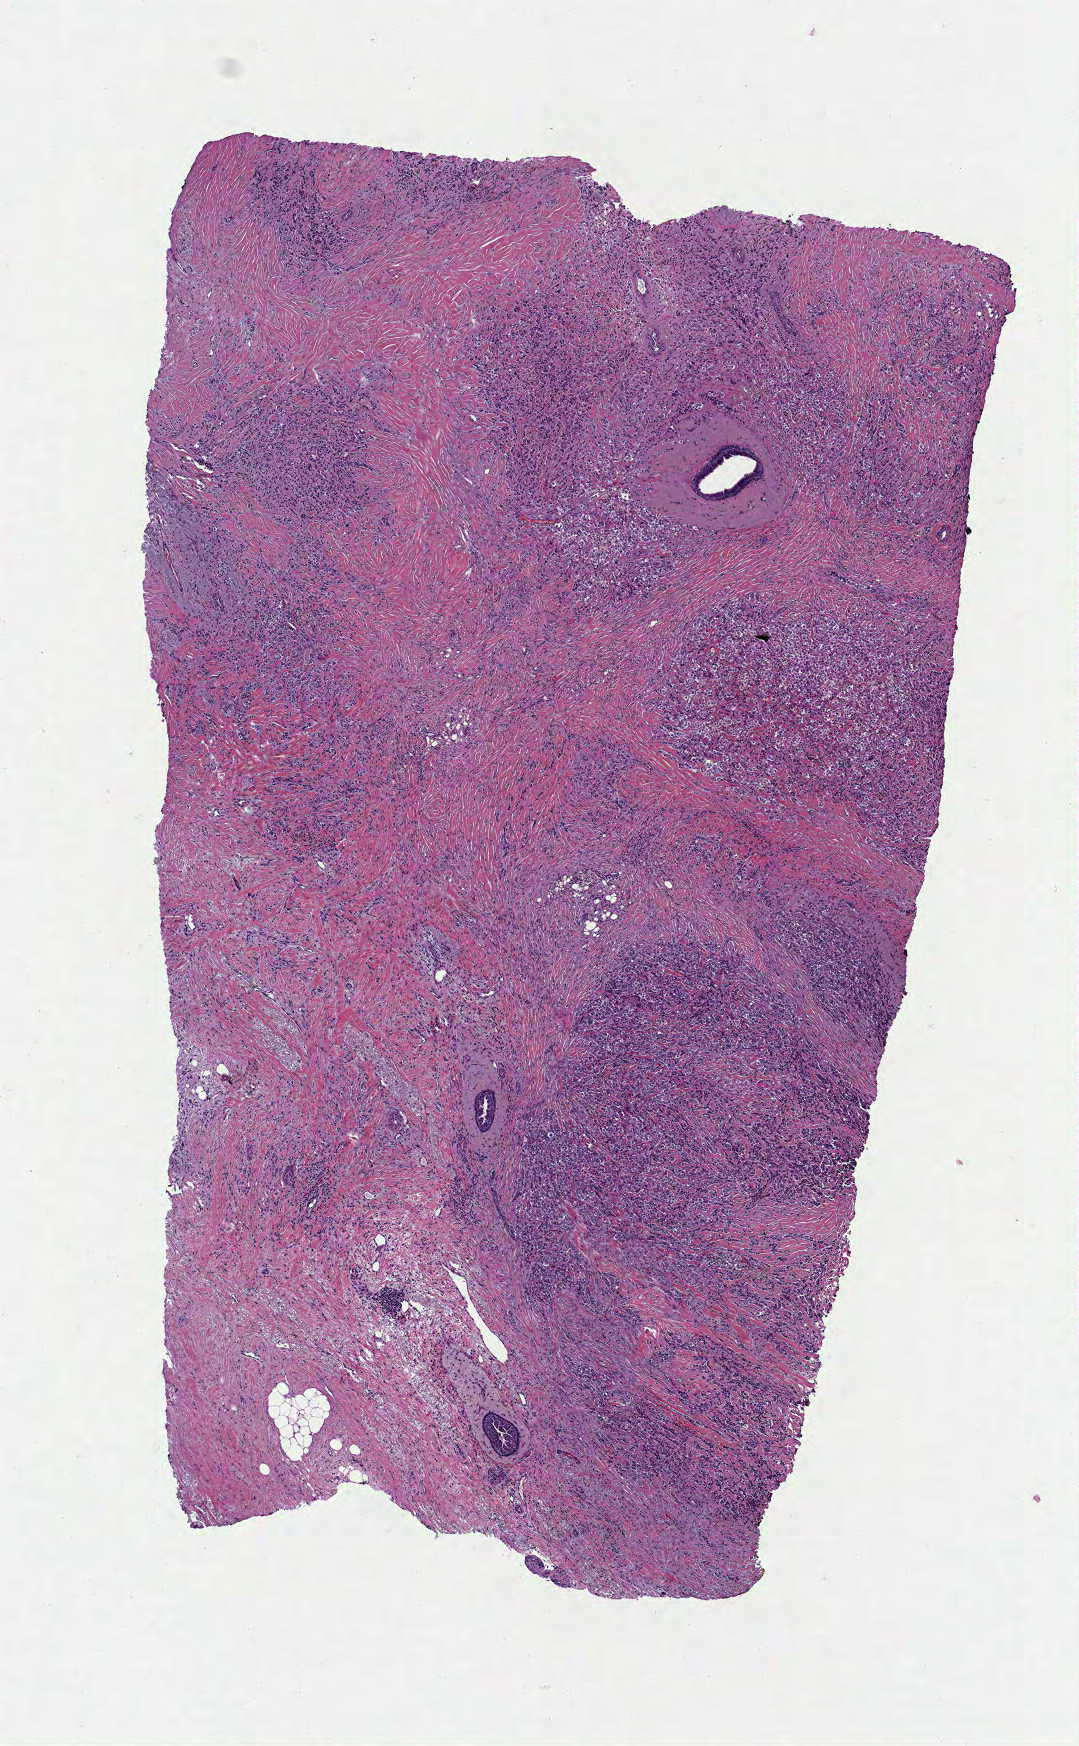
Whole-slide histology image, Hematoxylin and eosin (H&E) stained, whole scanned area (about 4.4 x 7.0 mm, from a 40x scan) shown as a low-resolution overview; FFPE section; sample: primary tumour, breast. Female, age 47 years at initial diagnosis.
Lymph nodes positive (case pathology): 1 of 1 examined. Histologic diagnosis: Infiltrating lobular mixed with other types of carcinoma. AJCC pathologic stage: IIB. TNM: T2 N1 MX. Laterality: right.